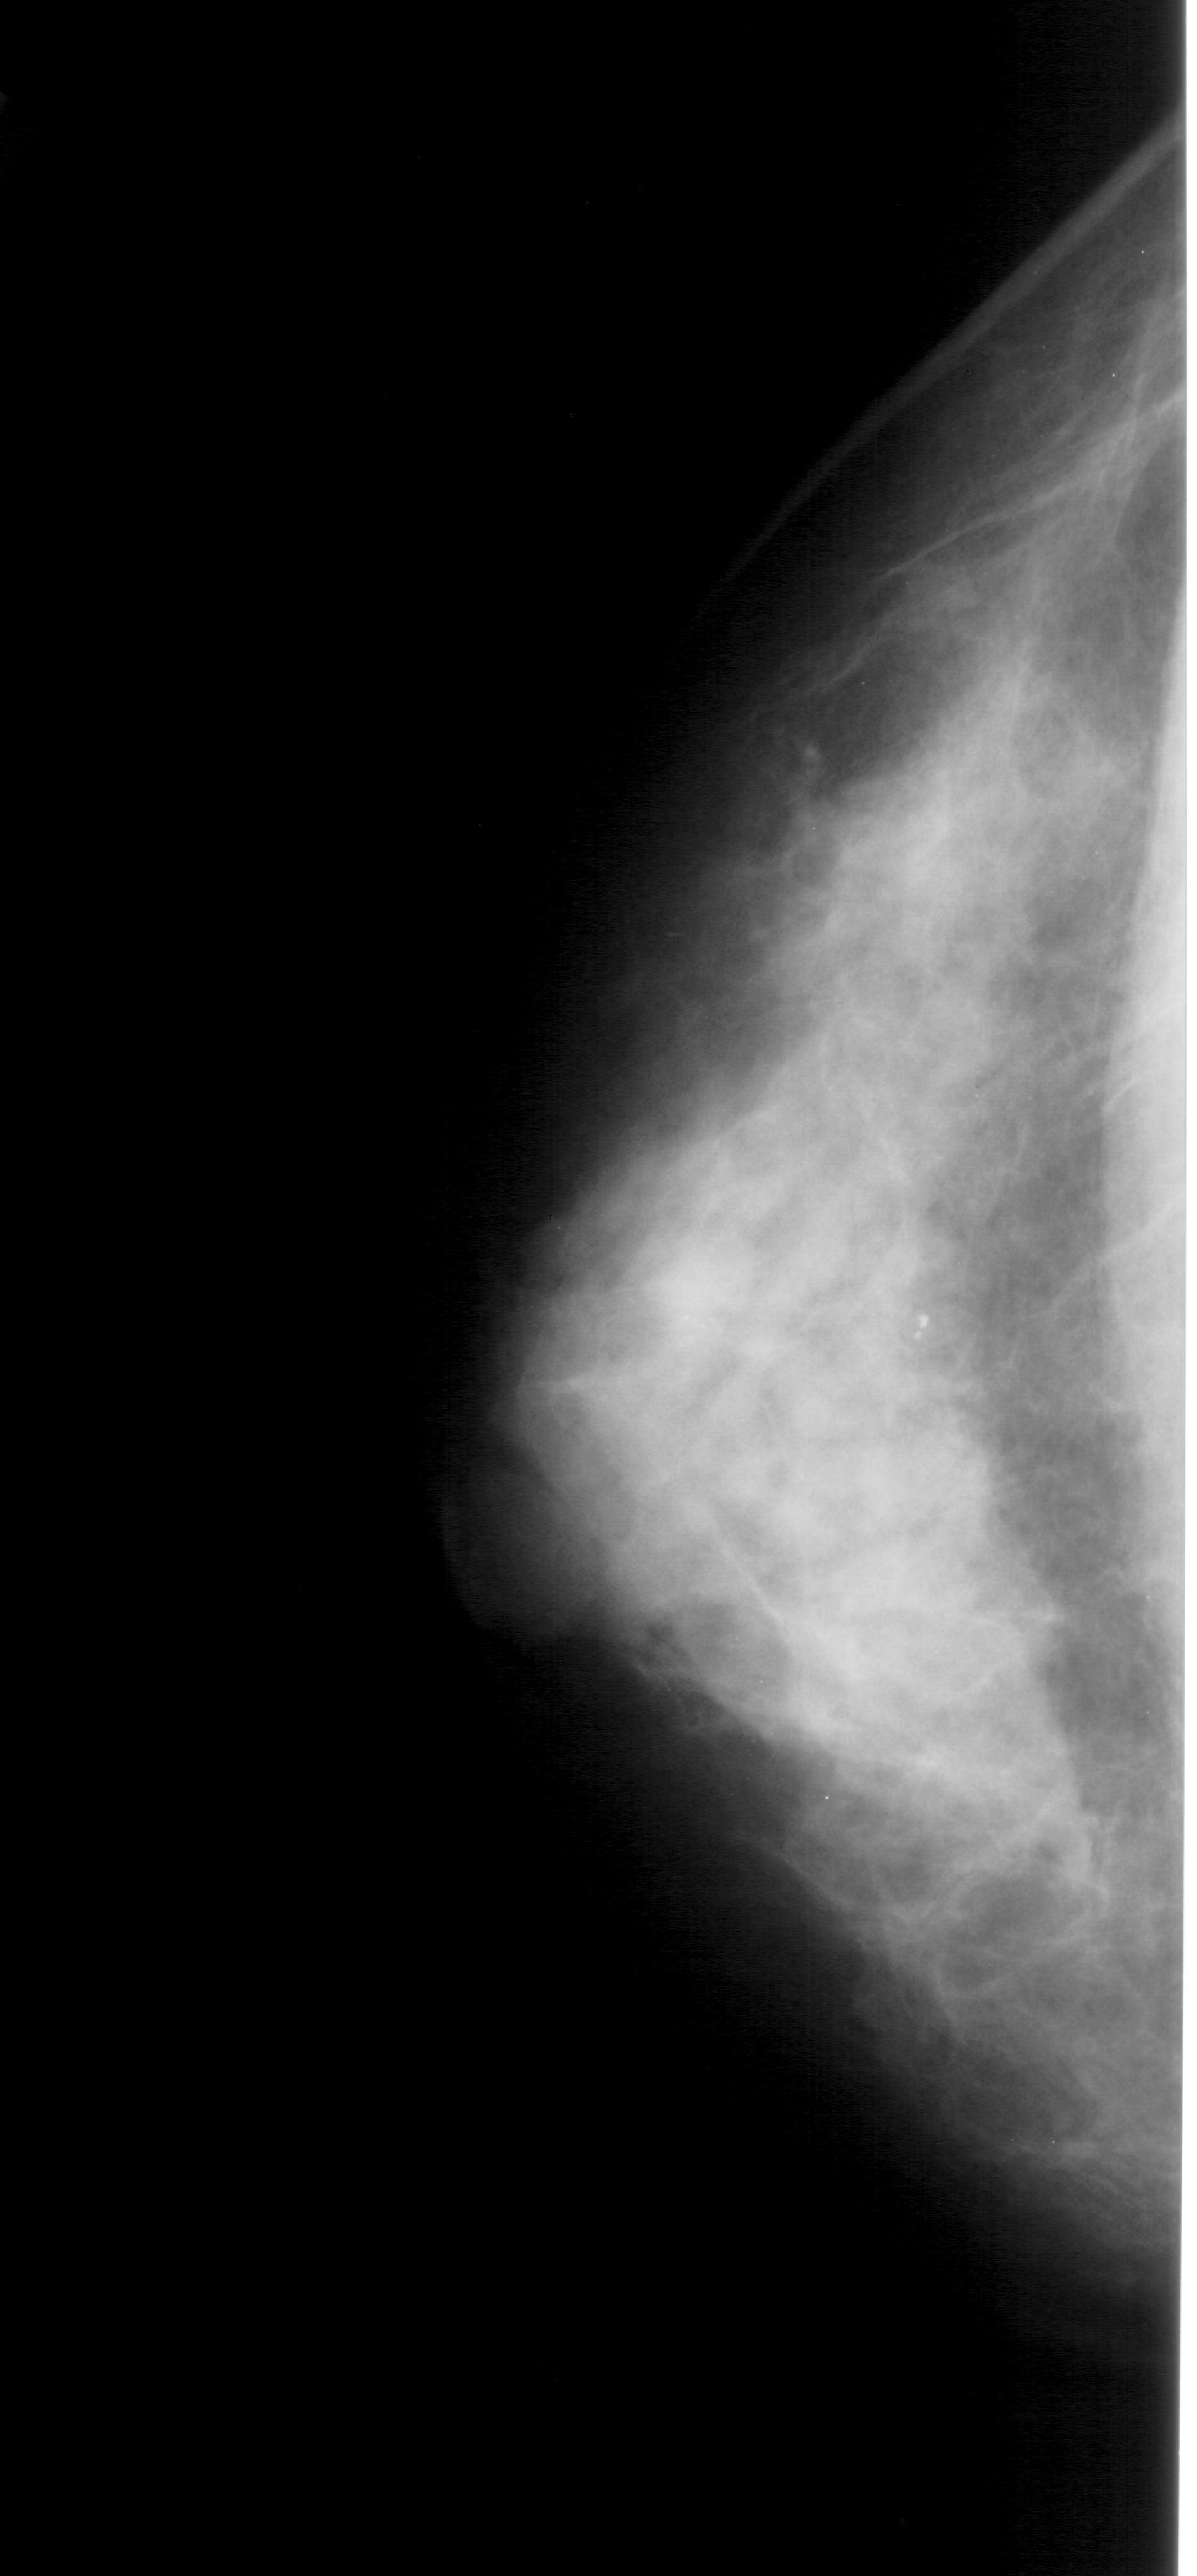
Digitized screen-film mammogram. Left breast. Craniocaudal (CC) view. BI-RADS breast density category 4 (scale 1–4). 1197 × 2576 image matrix.
Expert-marked regions of interest on this image (one box per marked abnormality):
- calcifications, morphology pleomorphic, distribution clustered; BI-RADS assessment category 4; pathology result (as recorded, not read from the image): benign: bounding box [x1, y1, x2, y2] px = [670, 1292, 729, 1355]